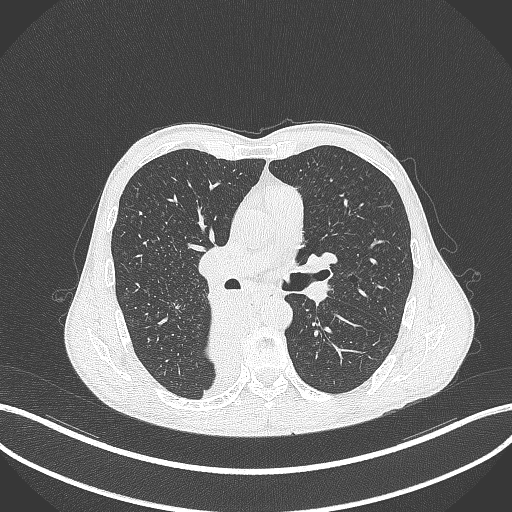
Chest CT, one axial slice; slice 218 of 371 in the series (ordered by position); reconstruction kernel B70f; 120 kVp; lung window (W 1500 / L -600 HU); 1 mm slice thickness; 512 × 512 image matrix. Patient: male, 58 years. Case-level facts recorded for this patient, not image findings: clinical TNM (as recorded): T3 N1 M1.
Outlined on this slice (bounding box drawn by a radiologist):
- lung tumour (recorded histology: squamous cell carcinoma): bounding box (x1, y1, x2, y2) in pixels: (205, 296, 248, 372)